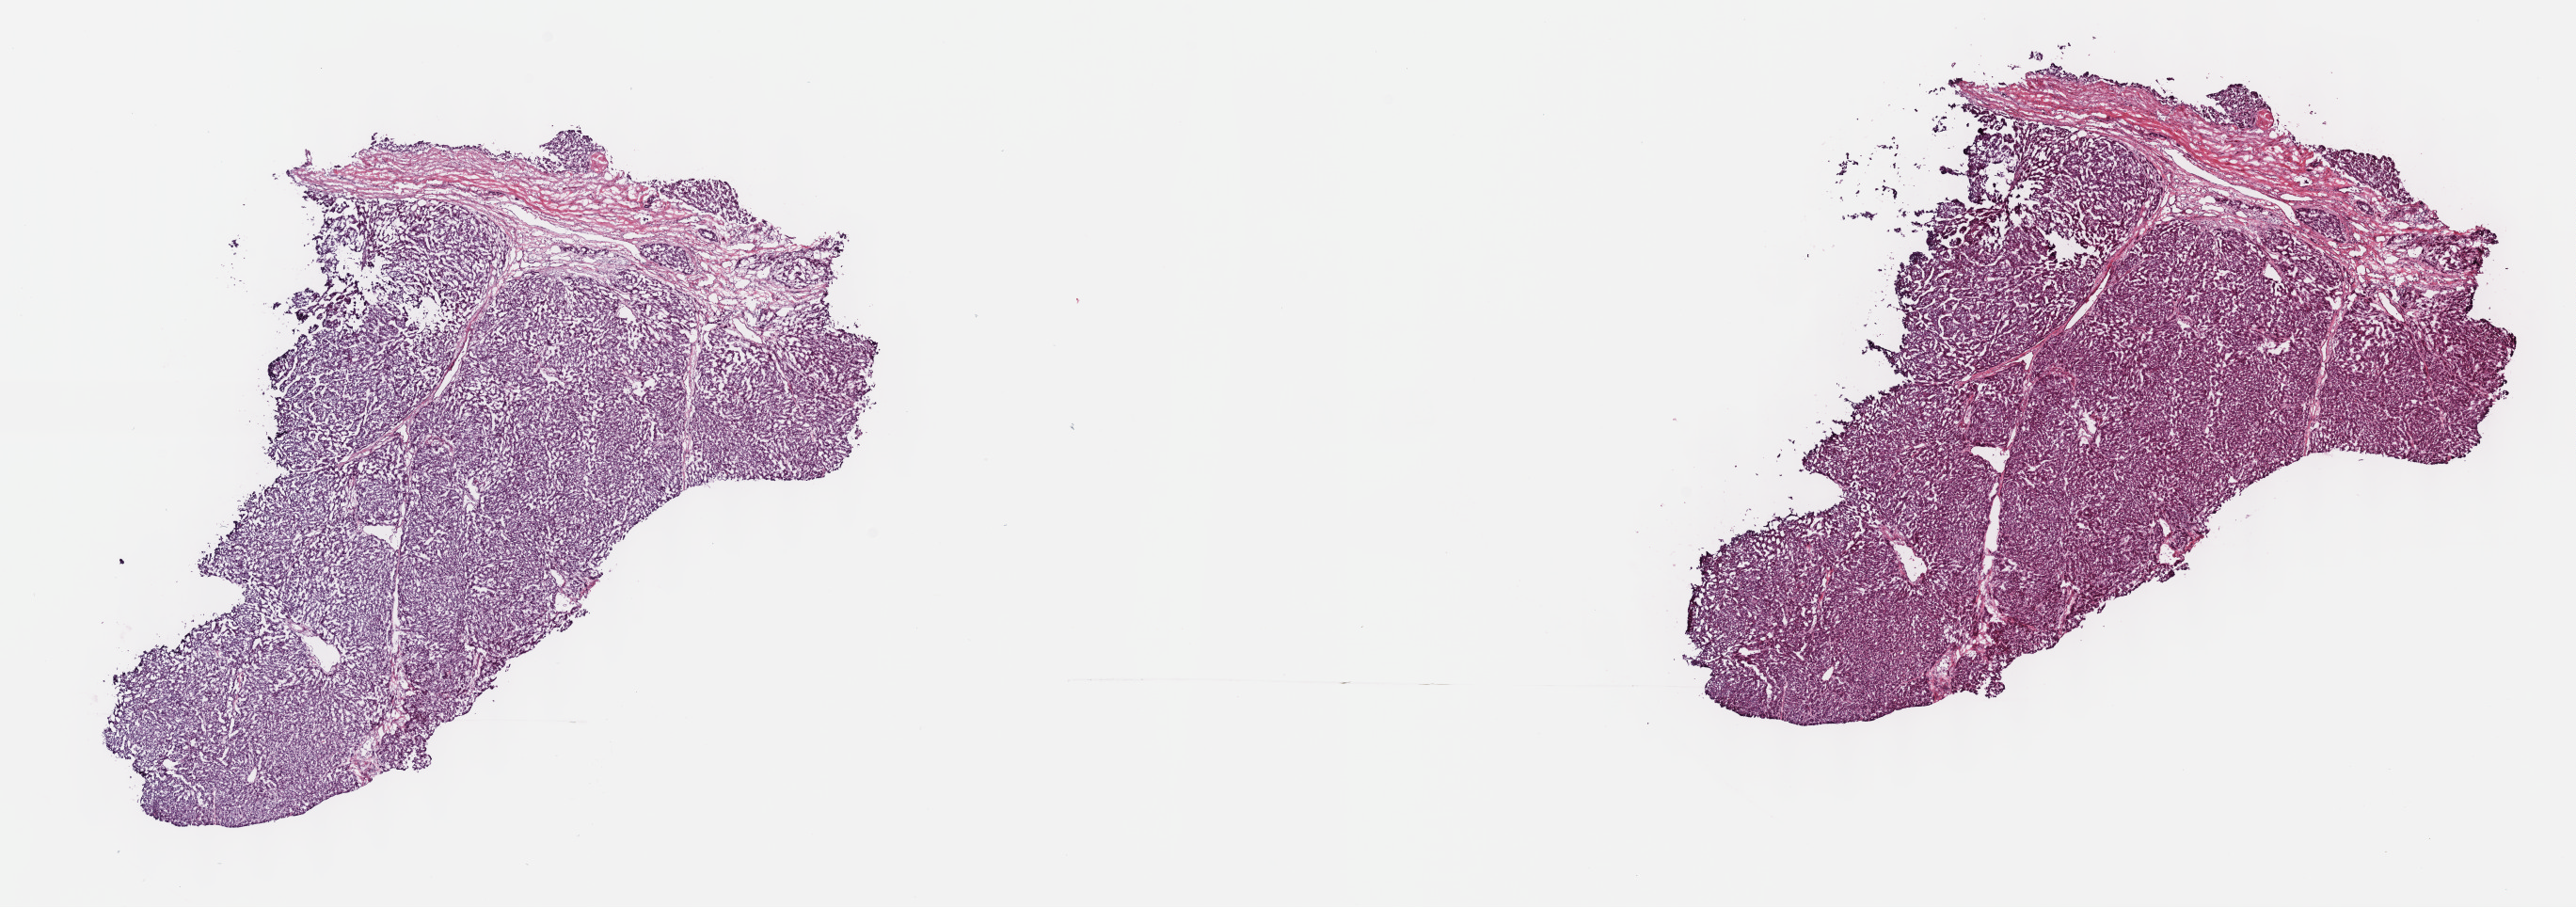
H&E-stained whole-slide image, a low-resolution overview of the entire scanned area, about 22.1 x 7.8 mm (slide scanned at 40x). Frozen section. Liver, primary tumour sample. Patient: female, age at initial diagnosis 20 years. Histologic grade: G3 (poorly differentiated). Composition of this section per pathologist review: tumour cells 100%, tumour nuclei 80%, normal cells 0%, stromal cells 0%, necrosis 0%. Inflammatory infiltration, as recorded: lymphocyte infiltration 2%, monocyte infiltration 0%, neutrophil infiltration 0%.
AJCC pathologic stage: II (7th edition). Histologic diagnosis: Hepatocellular carcinoma, NOS.